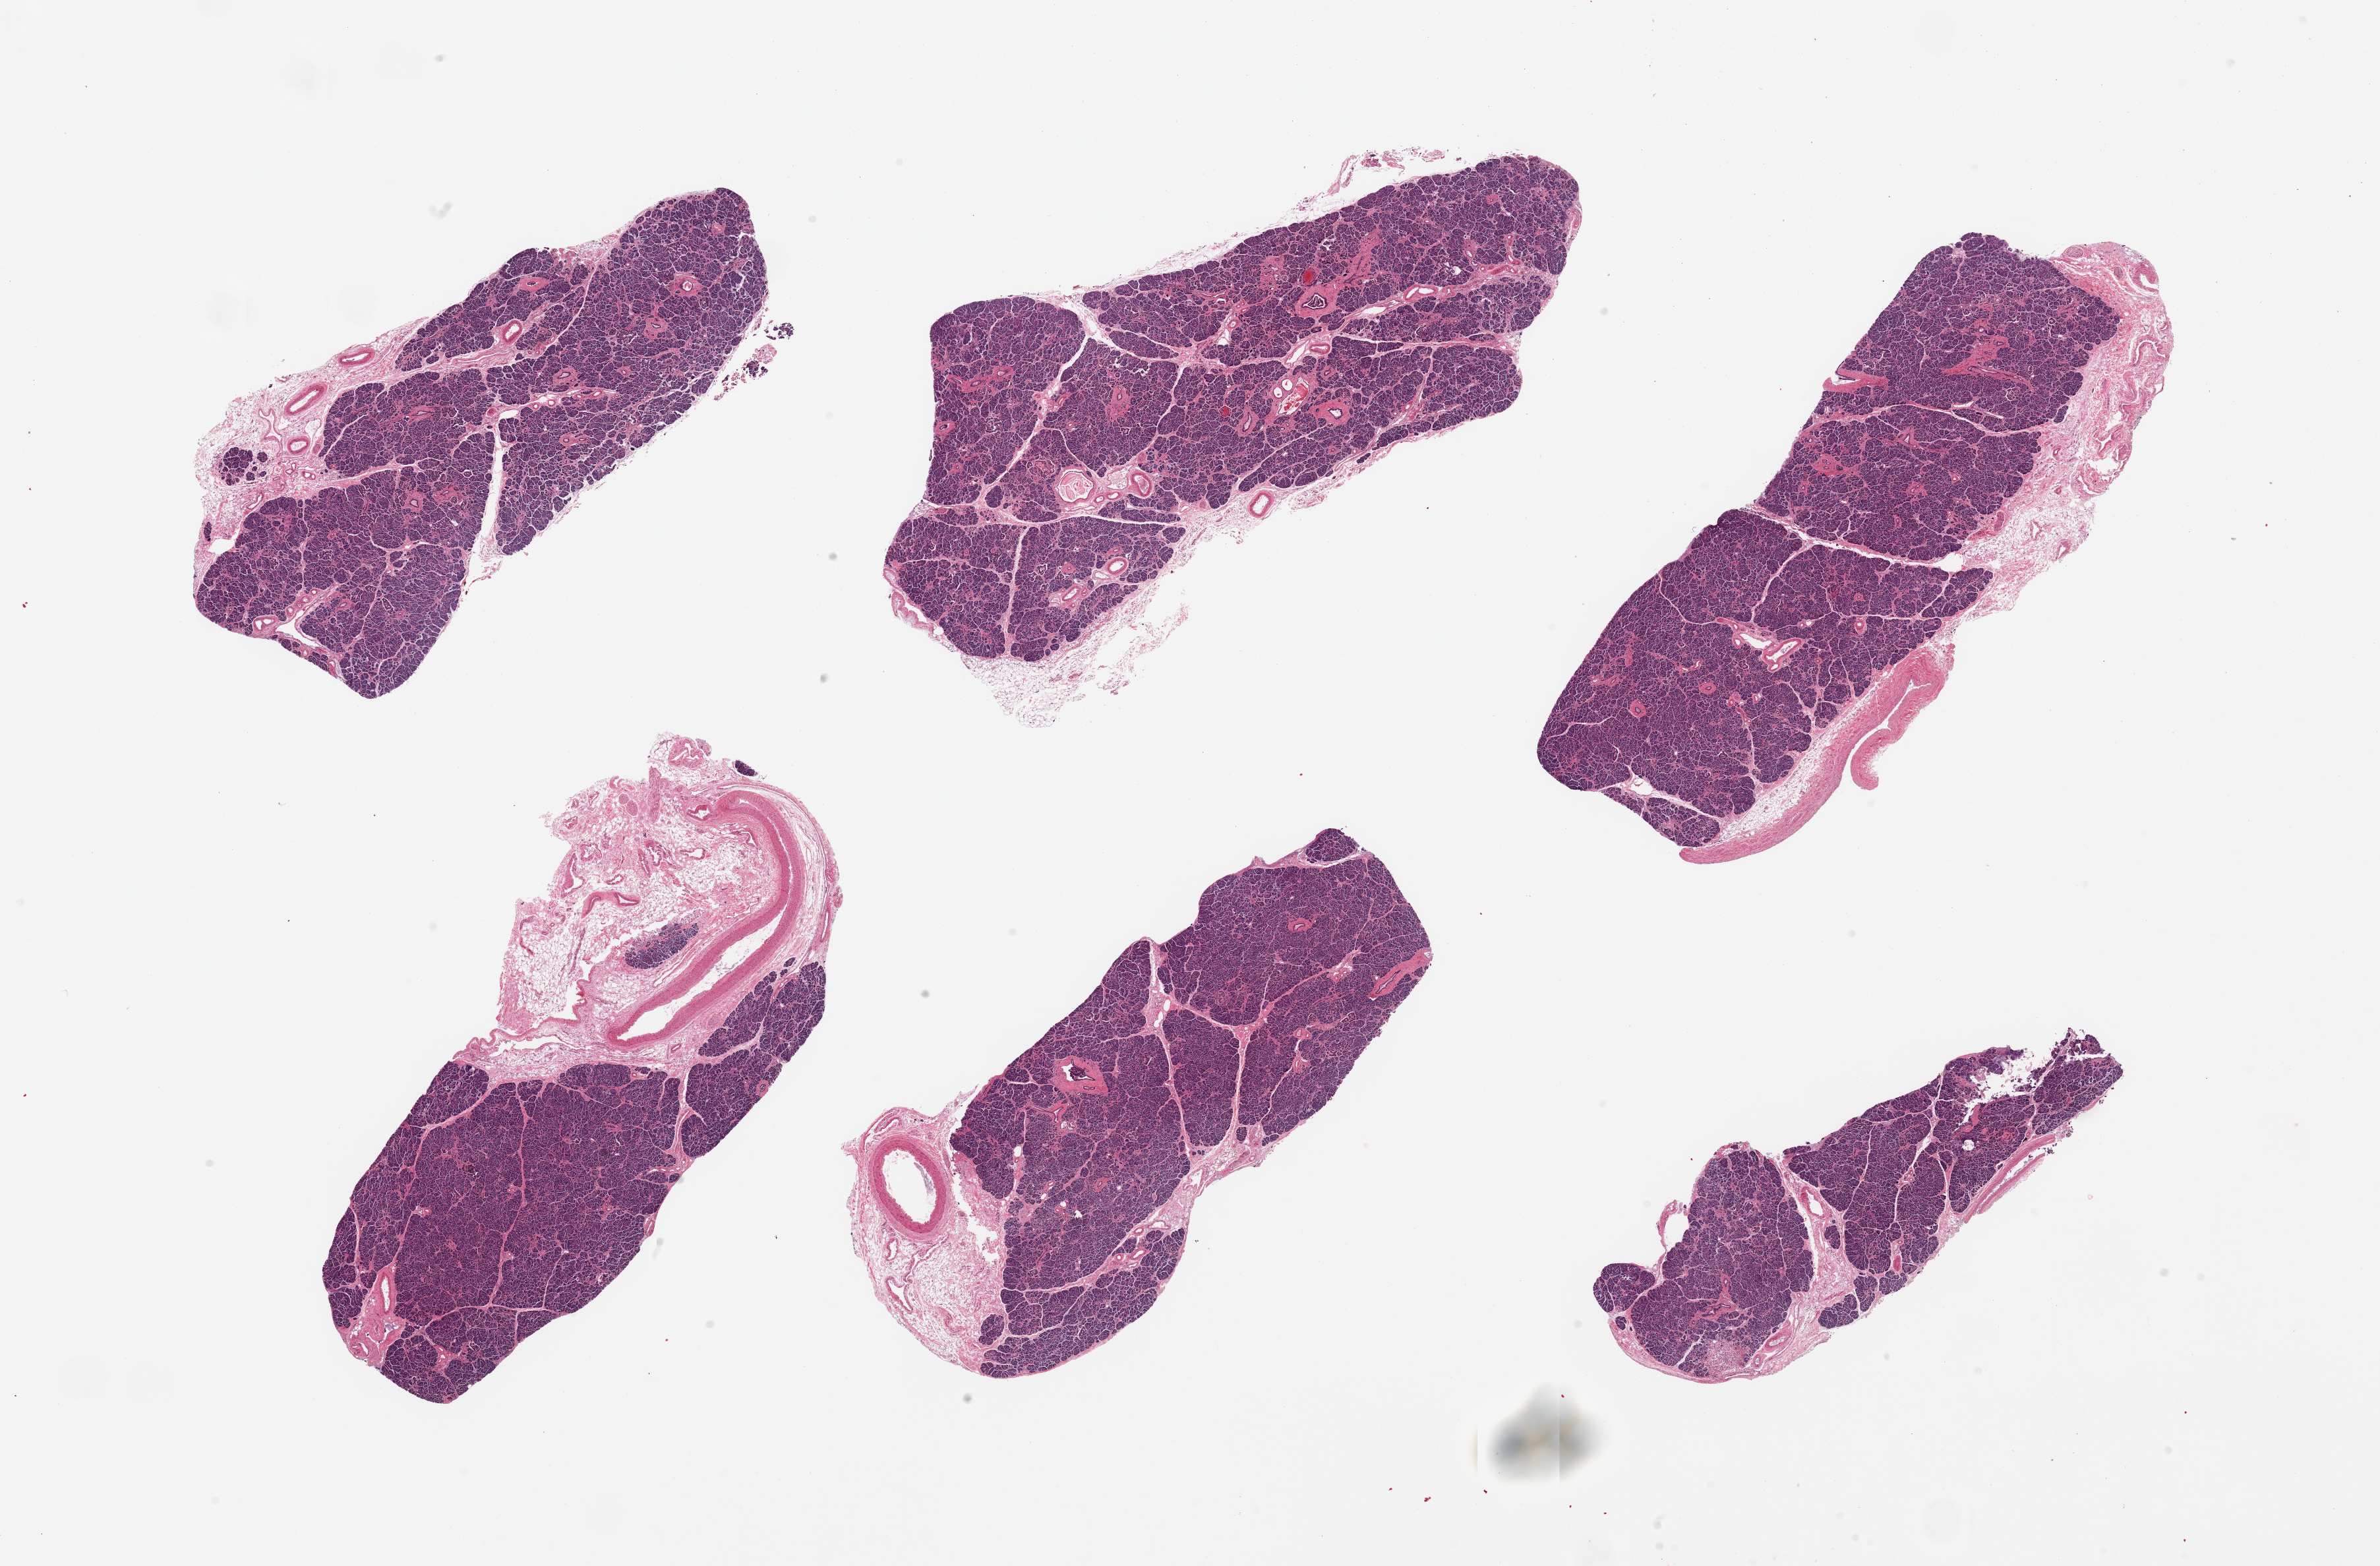
Digitized haematoxylin and eosin-stained section, low-resolution overview of the scanned area, about 28.5 x 18.8 mm. PAXgene-fixed paraffin-embedded (PFPE) section. Target tissue: pancreas. Donor tissue sample. Donor: male.
Pathologist's review note for this sample: 6 pieces; PANCREAS not aorta; 10% to 40% peripancreatic stroma.